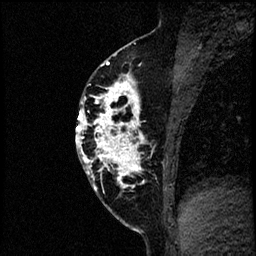
Breast MRI (dynamic contrast-enhanced), one sagittal slice; slice 32 of 60 in the series (ordered by position); dynamic contrast-enhanced study with each time point stored as its own series, time point 2 of 4 at this slice position (early post-contrast, ordered by acquisition time); 1.5 T; TE 4.2 ms, TR 17.6 ms; 2 mm slice thickness; 256 × 256 image matrix, field of view 200 × 200 mm. Patient: female, 40 years. Case-level facts recorded for this patient, not image findings: setting: breast cancer imaged before/during neoadjuvant chemotherapy; receptor status: HER2-positive.
Structures marked on this image (semi-automatic segmentation, software-assisted and operator-edited):
- analysis volume of interest (the breast-tissue region the enhancement analysis was run in; not a lesion): bounding box (x1, y1, x2, y2) in pixels: (77, 56, 197, 205)
- tumour enhancement mask (voxels above the 100 % enhancement threshold inside the analysis volume of interest): (77, 60, 147, 188)